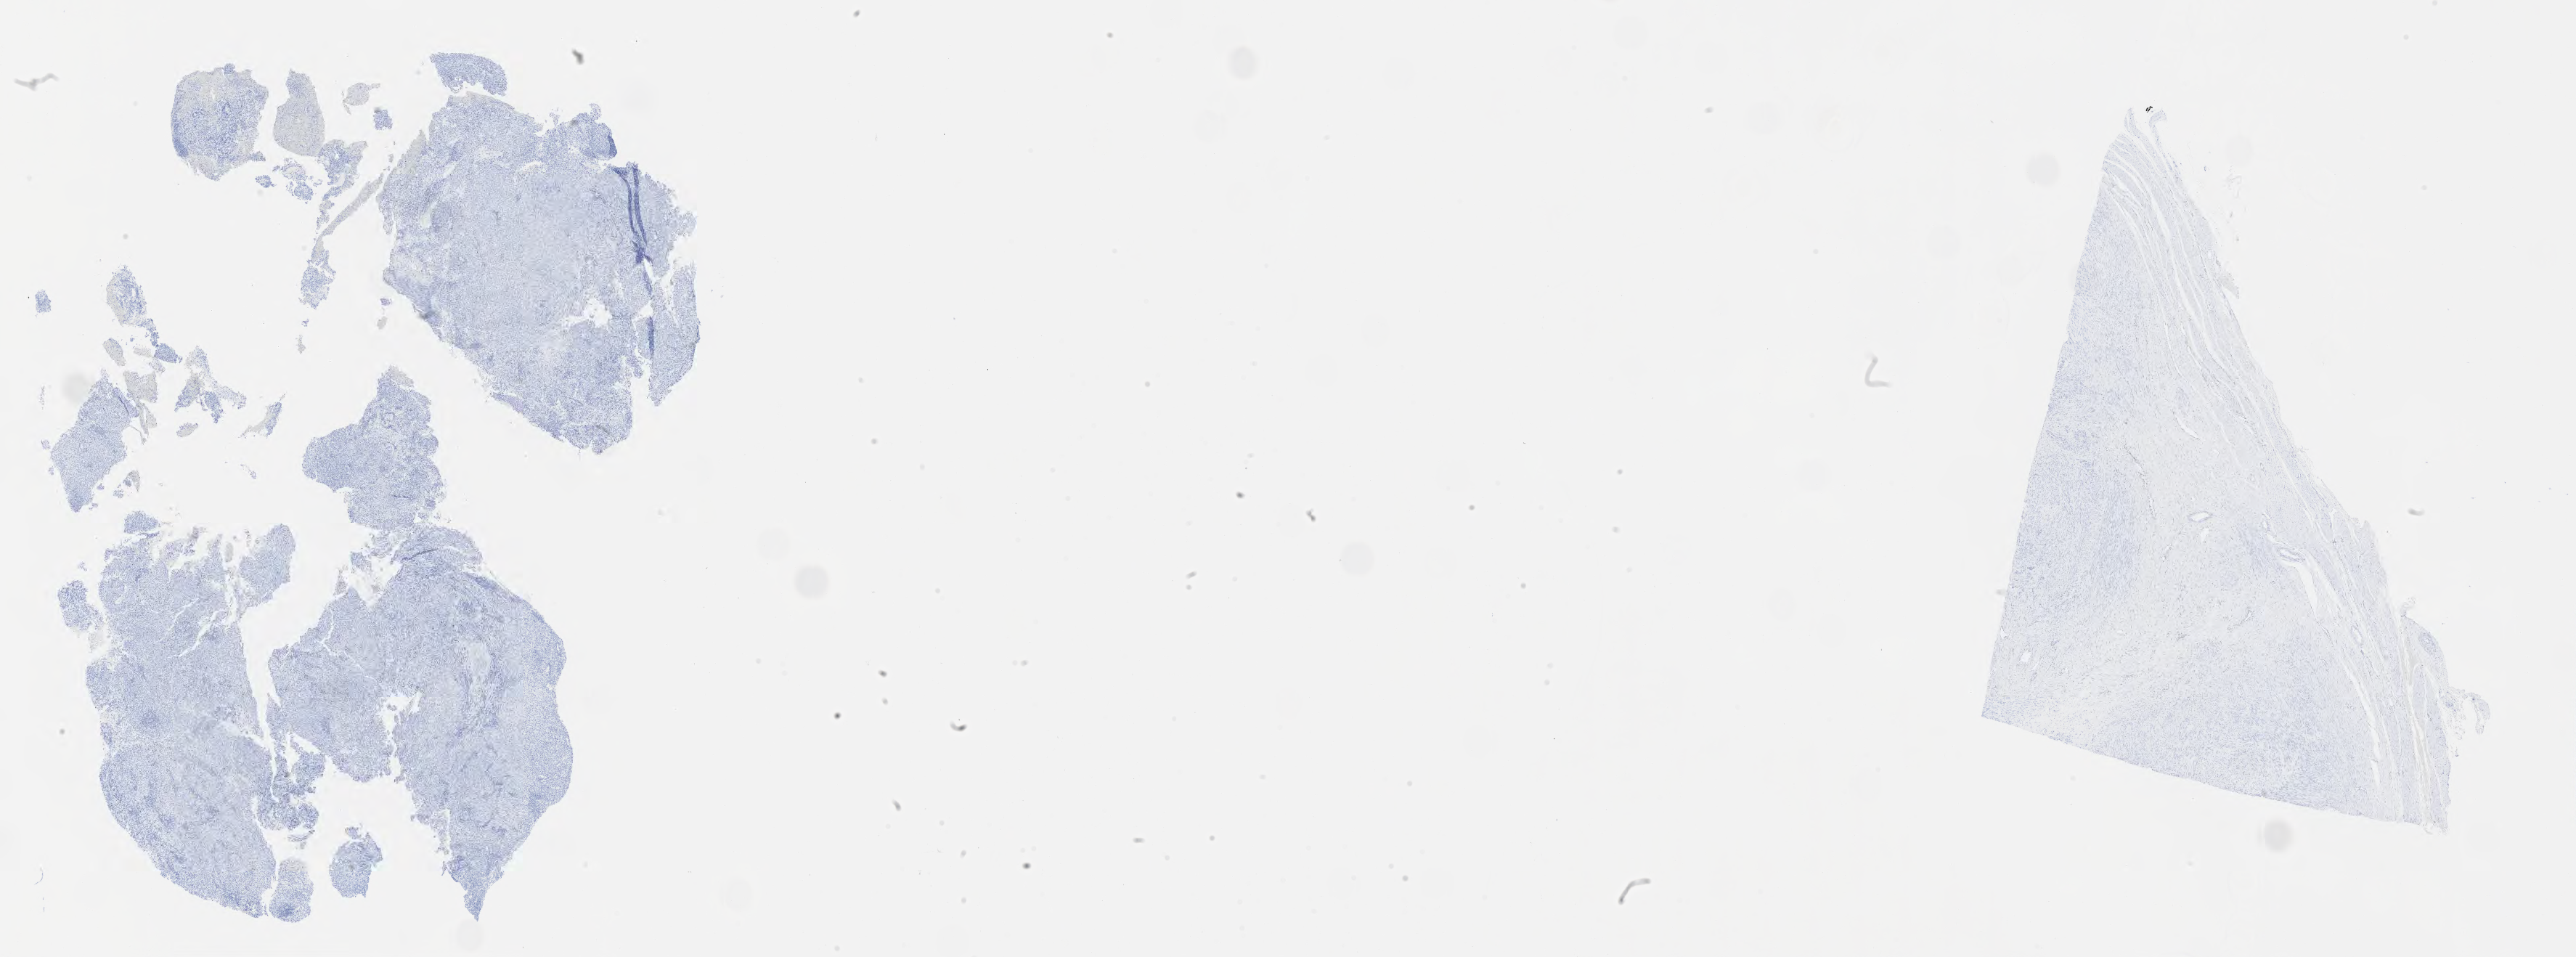
Whole-slide image, immunohistochemical stain for progesterone receptor (PR), whole scanned area (about 28.7 x 10.7 mm) shown as a low-resolution overview; specimen: tumor tissue; site: cervix. Female patient, age 70 years.
Histologic diagnosis: Squamous cell carcinoma, large cell, nonkeratinizing, NOS.